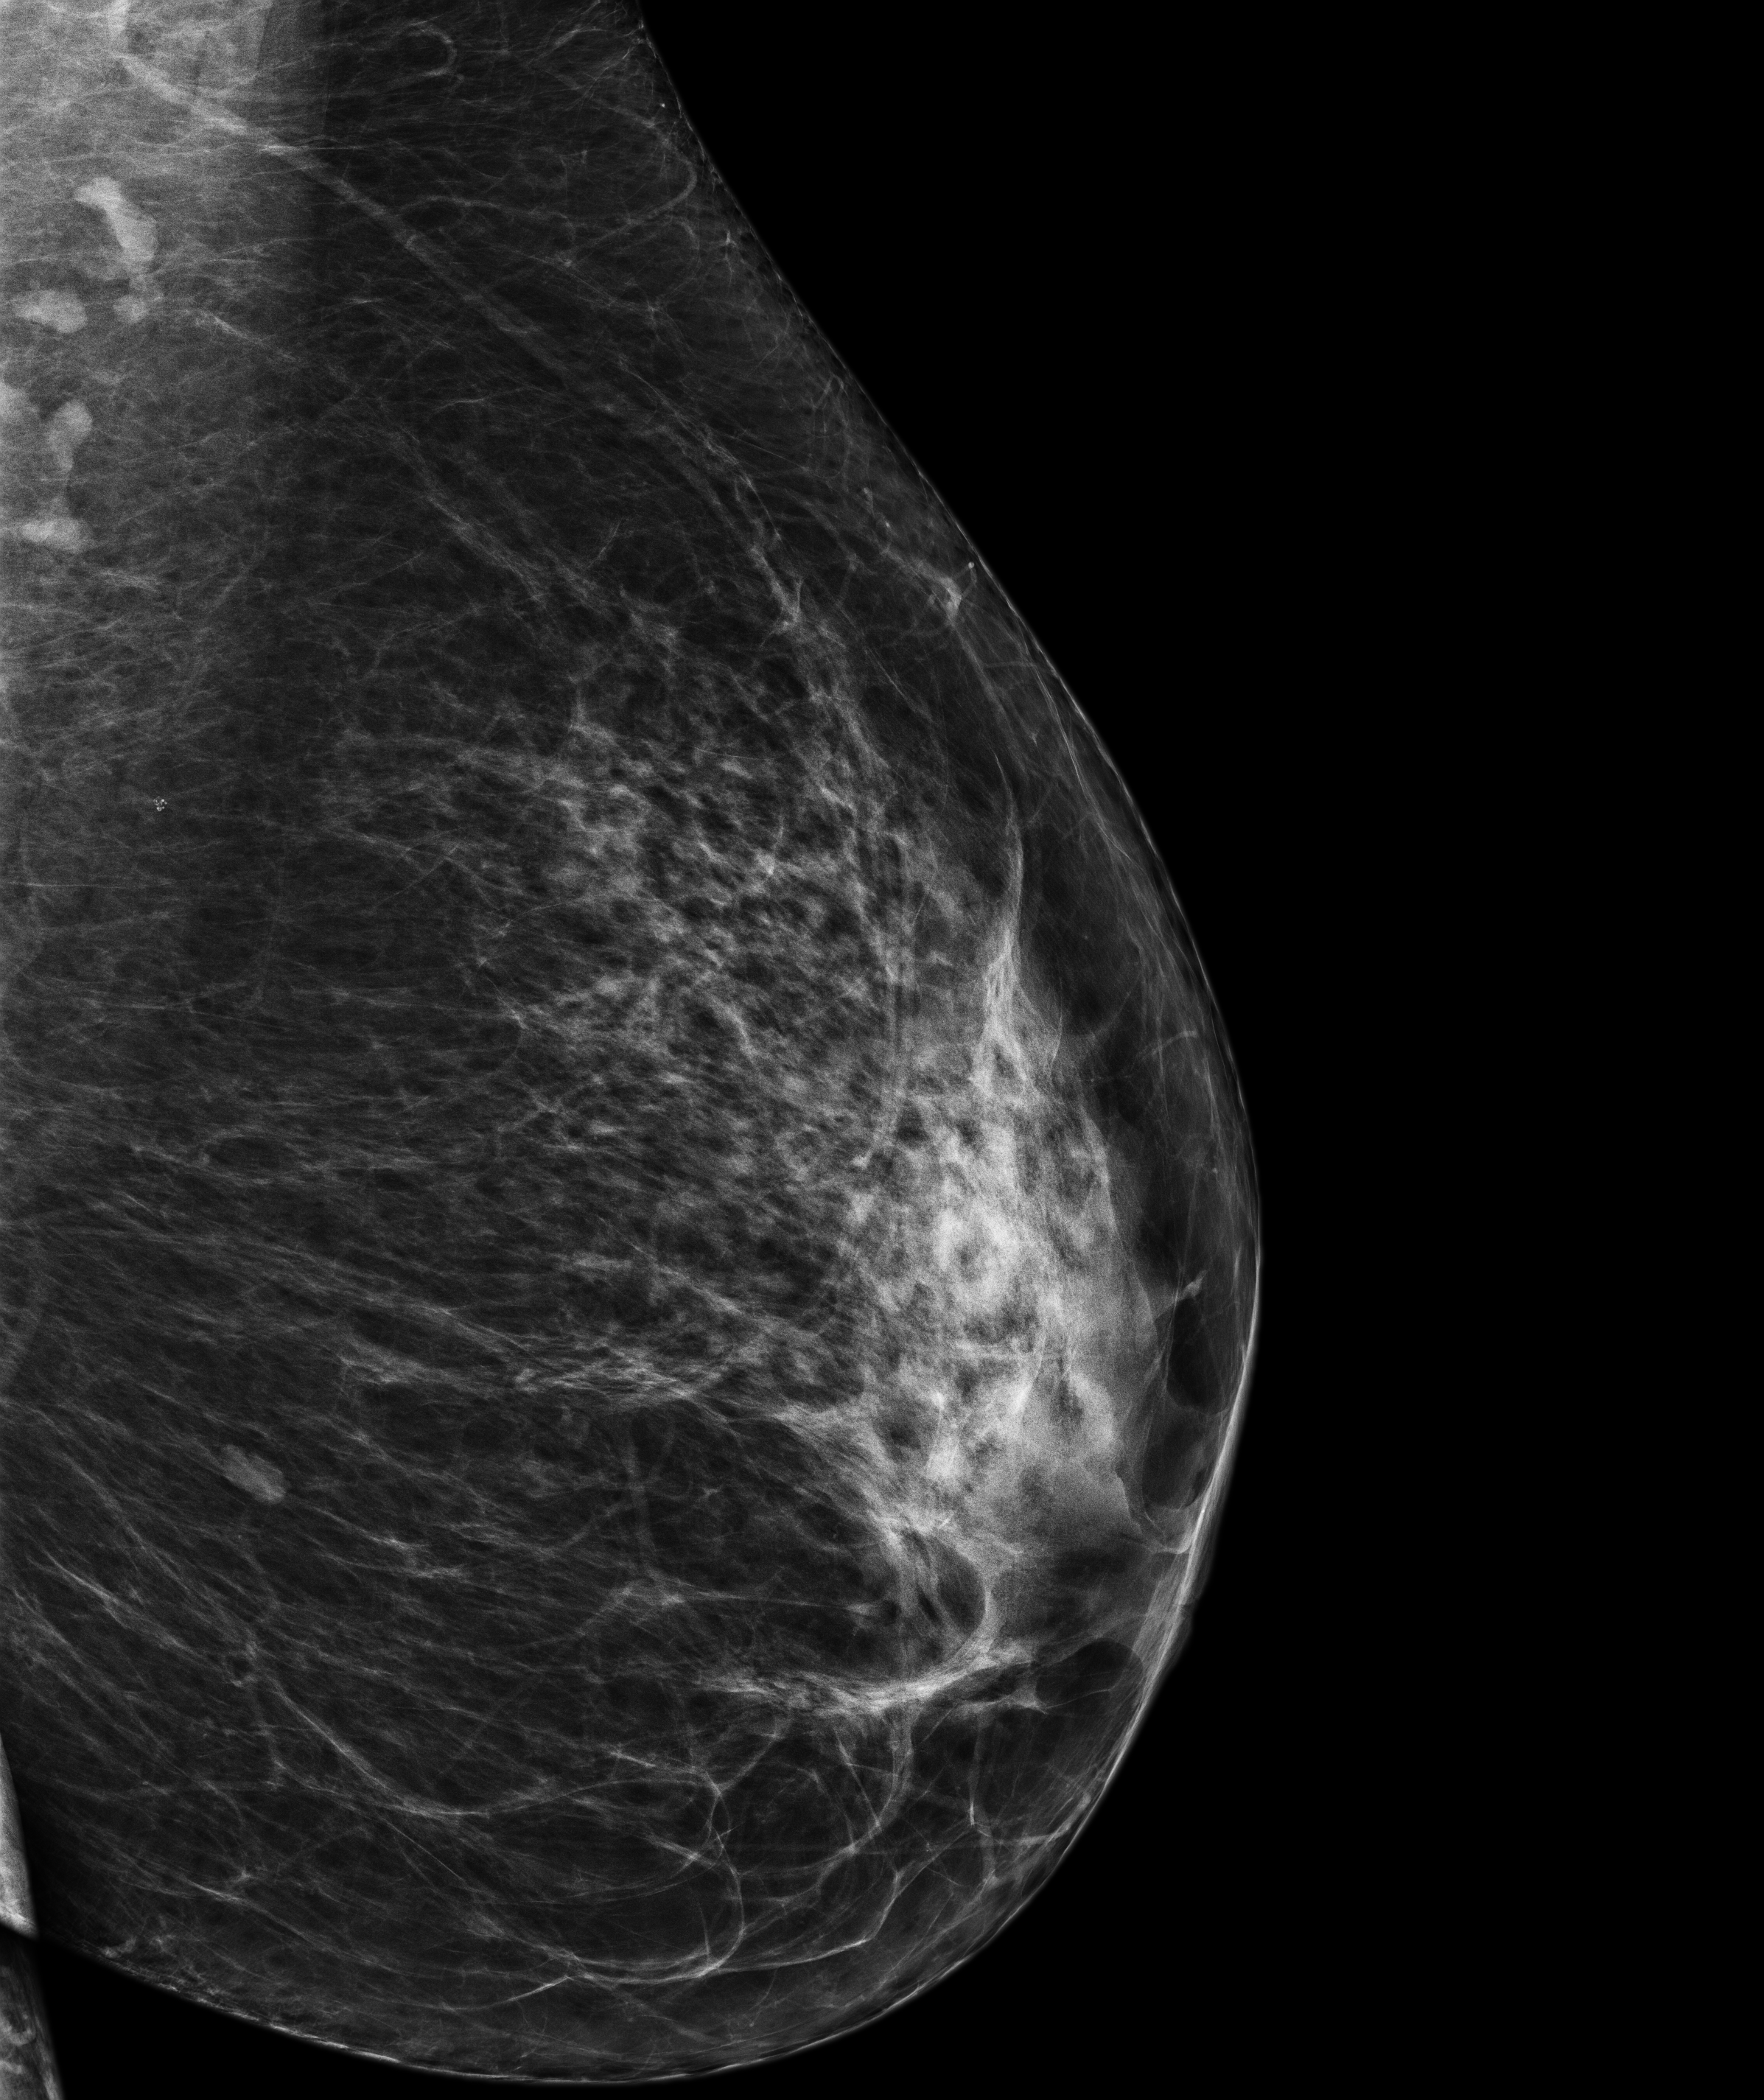
Screening examination, compressed breast thickness 70.8 mm. Patient: female, 57 years.
Image type: full-field digital mammogram. Breast: left. Projection: mediolateral oblique (MLO) view.